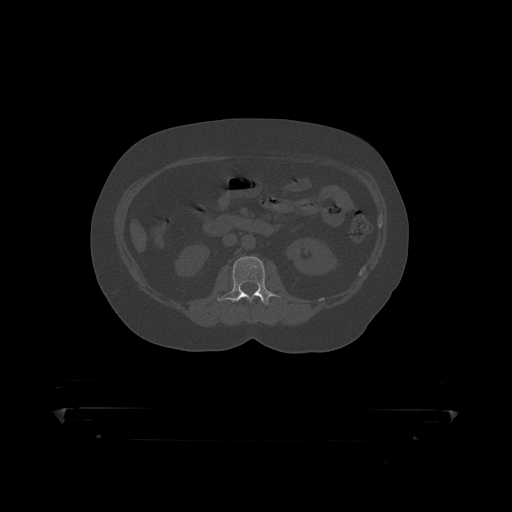
CT including the spine, one axial slice. Slice 121 of 390 in the series (ordered by position). Reconstruction kernel STANDARD. 120 kVp. Bone window (W 1800 / L 400 HU). 1.25 mm slice thickness. 512 × 512 image matrix, field of view 650 × 650 mm. Male patient, age 60 years. From the clinical record (not read from this slice): primary cancer: prostate.
Annotated regions visible in this slice (semi-automatic segmentation, software-assisted and operator-edited):
- L1 vertebra: bounding box [x1, y1, x2, y2] px = [260, 301, 263, 304]
- L2 vertebra: [218, 257, 278, 306]